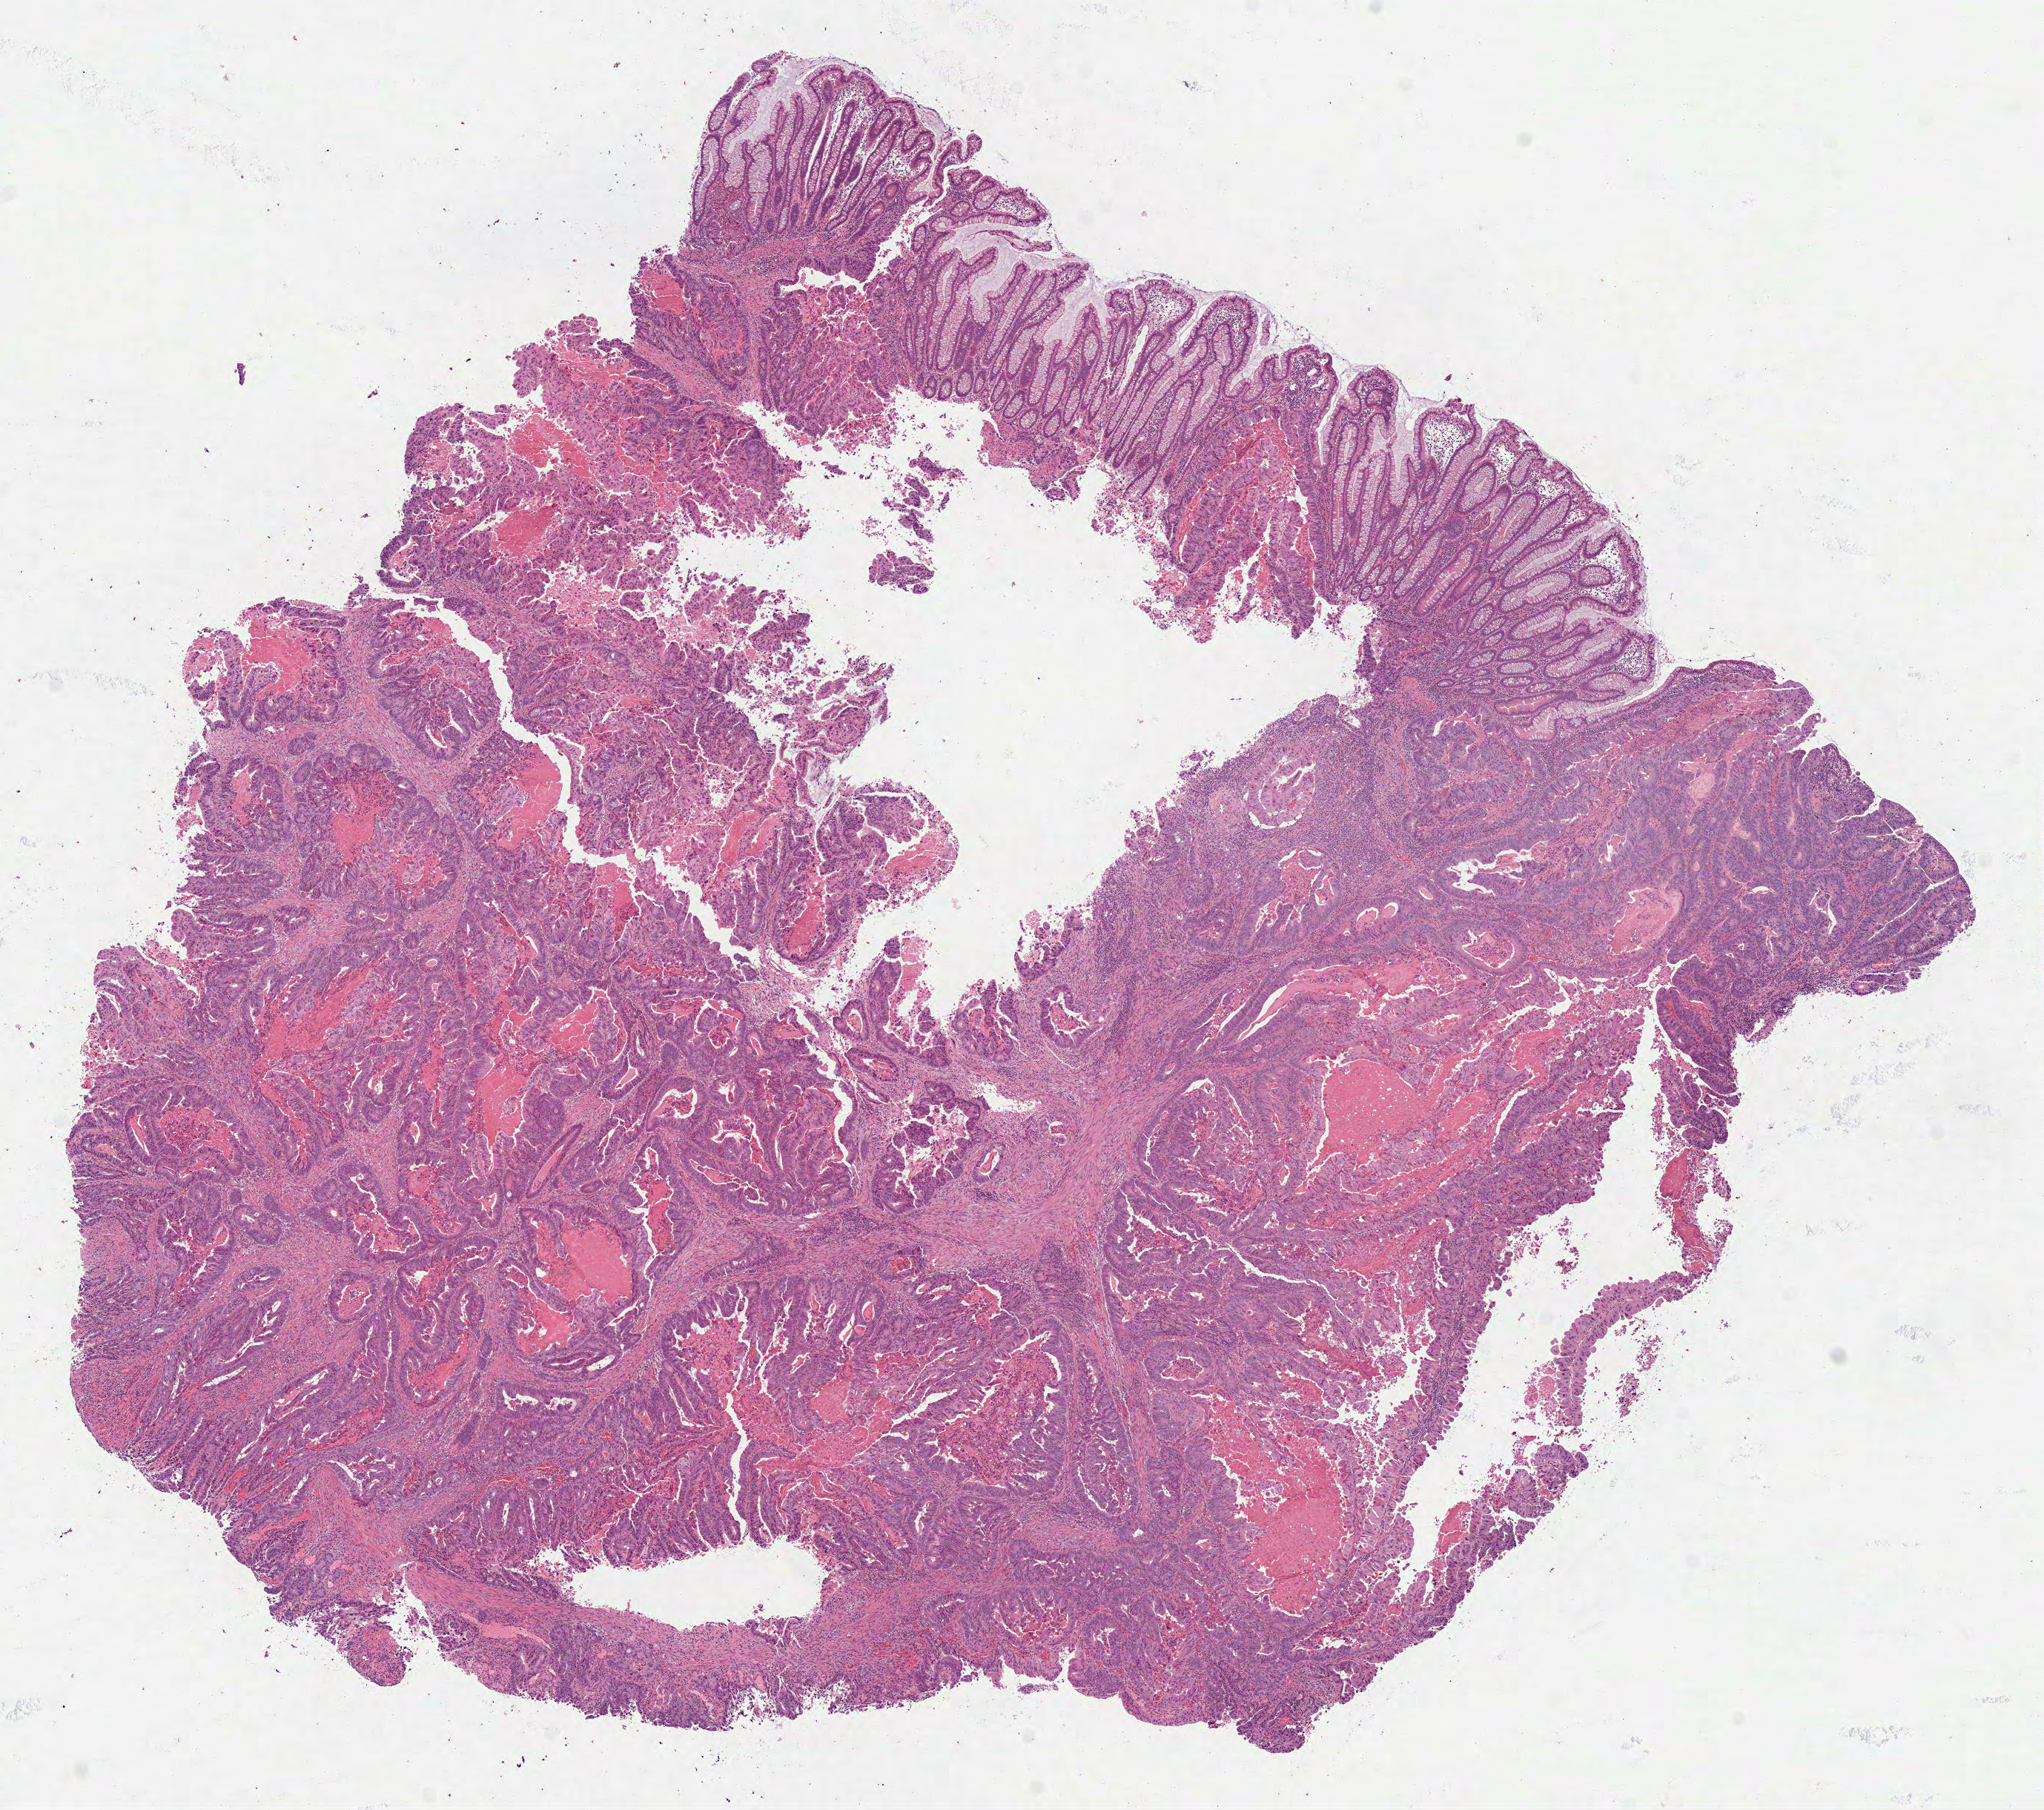
Hematoxylin and eosin (H&E) stained whole-slide image, whole scanned area (about 11.1 x 9.8 mm) shown as a low-resolution overview. Formalin-fixed paraffin-embedded (FFPE) diagnostic section. Primary tumour sample from the colon. Patient: male, age at initial diagnosis 73 years.
- pathologic diagnosis: Adenocarcinoma, NOS (ascending colon)
- AJCC pathologic stage: IIIB (7th edition)
- lymph nodes positive (case pathology): 2 of 18 examined
- TNM: T3 N1b M0